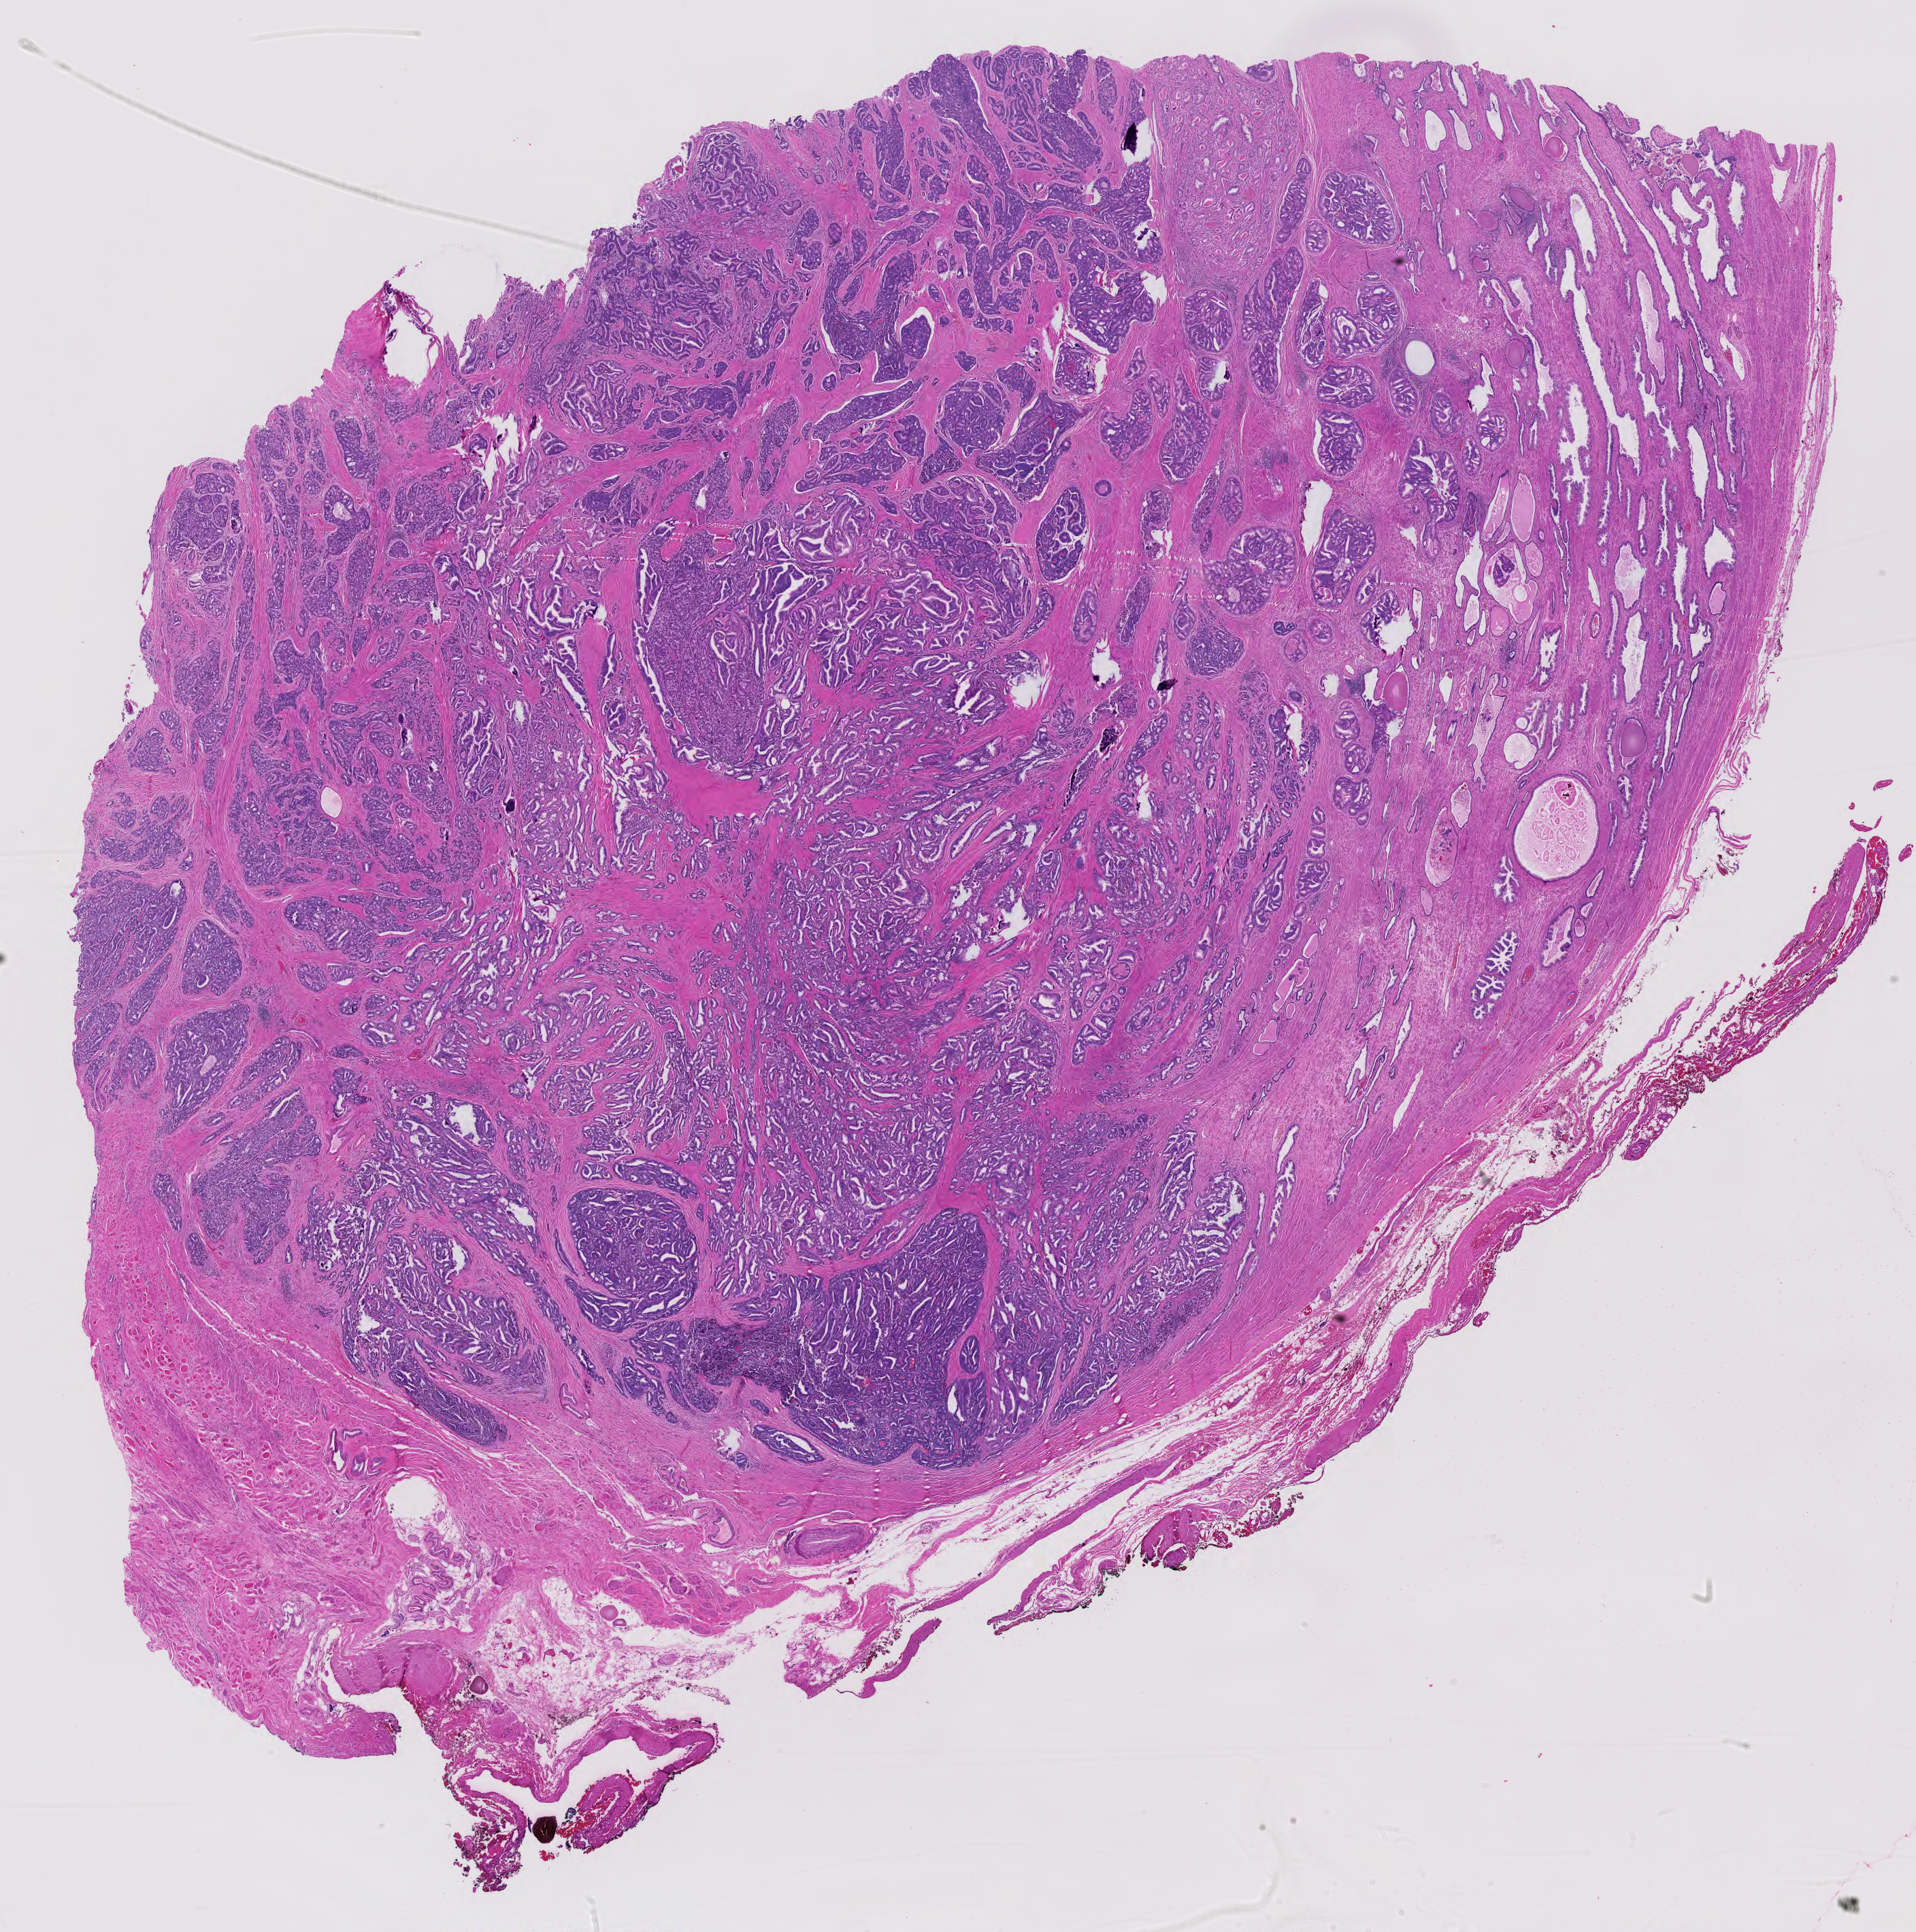
Whole-slide histology image, H&E-stained, a low-resolution overview of the entire scanned area, about 20.4 x 20.6 mm (slide scanned at 40x); formalin-fixed paraffin-embedded (FFPE) diagnostic section; primary tumour sample from the prostate. Male, age 63 years at initial diagnosis. Gleason score: 9 (4+5).
* pathologic diagnosis: Adenocarcinoma, NOS (prostate gland)
* lymph nodes positive (case pathology): 1 of 15 examined